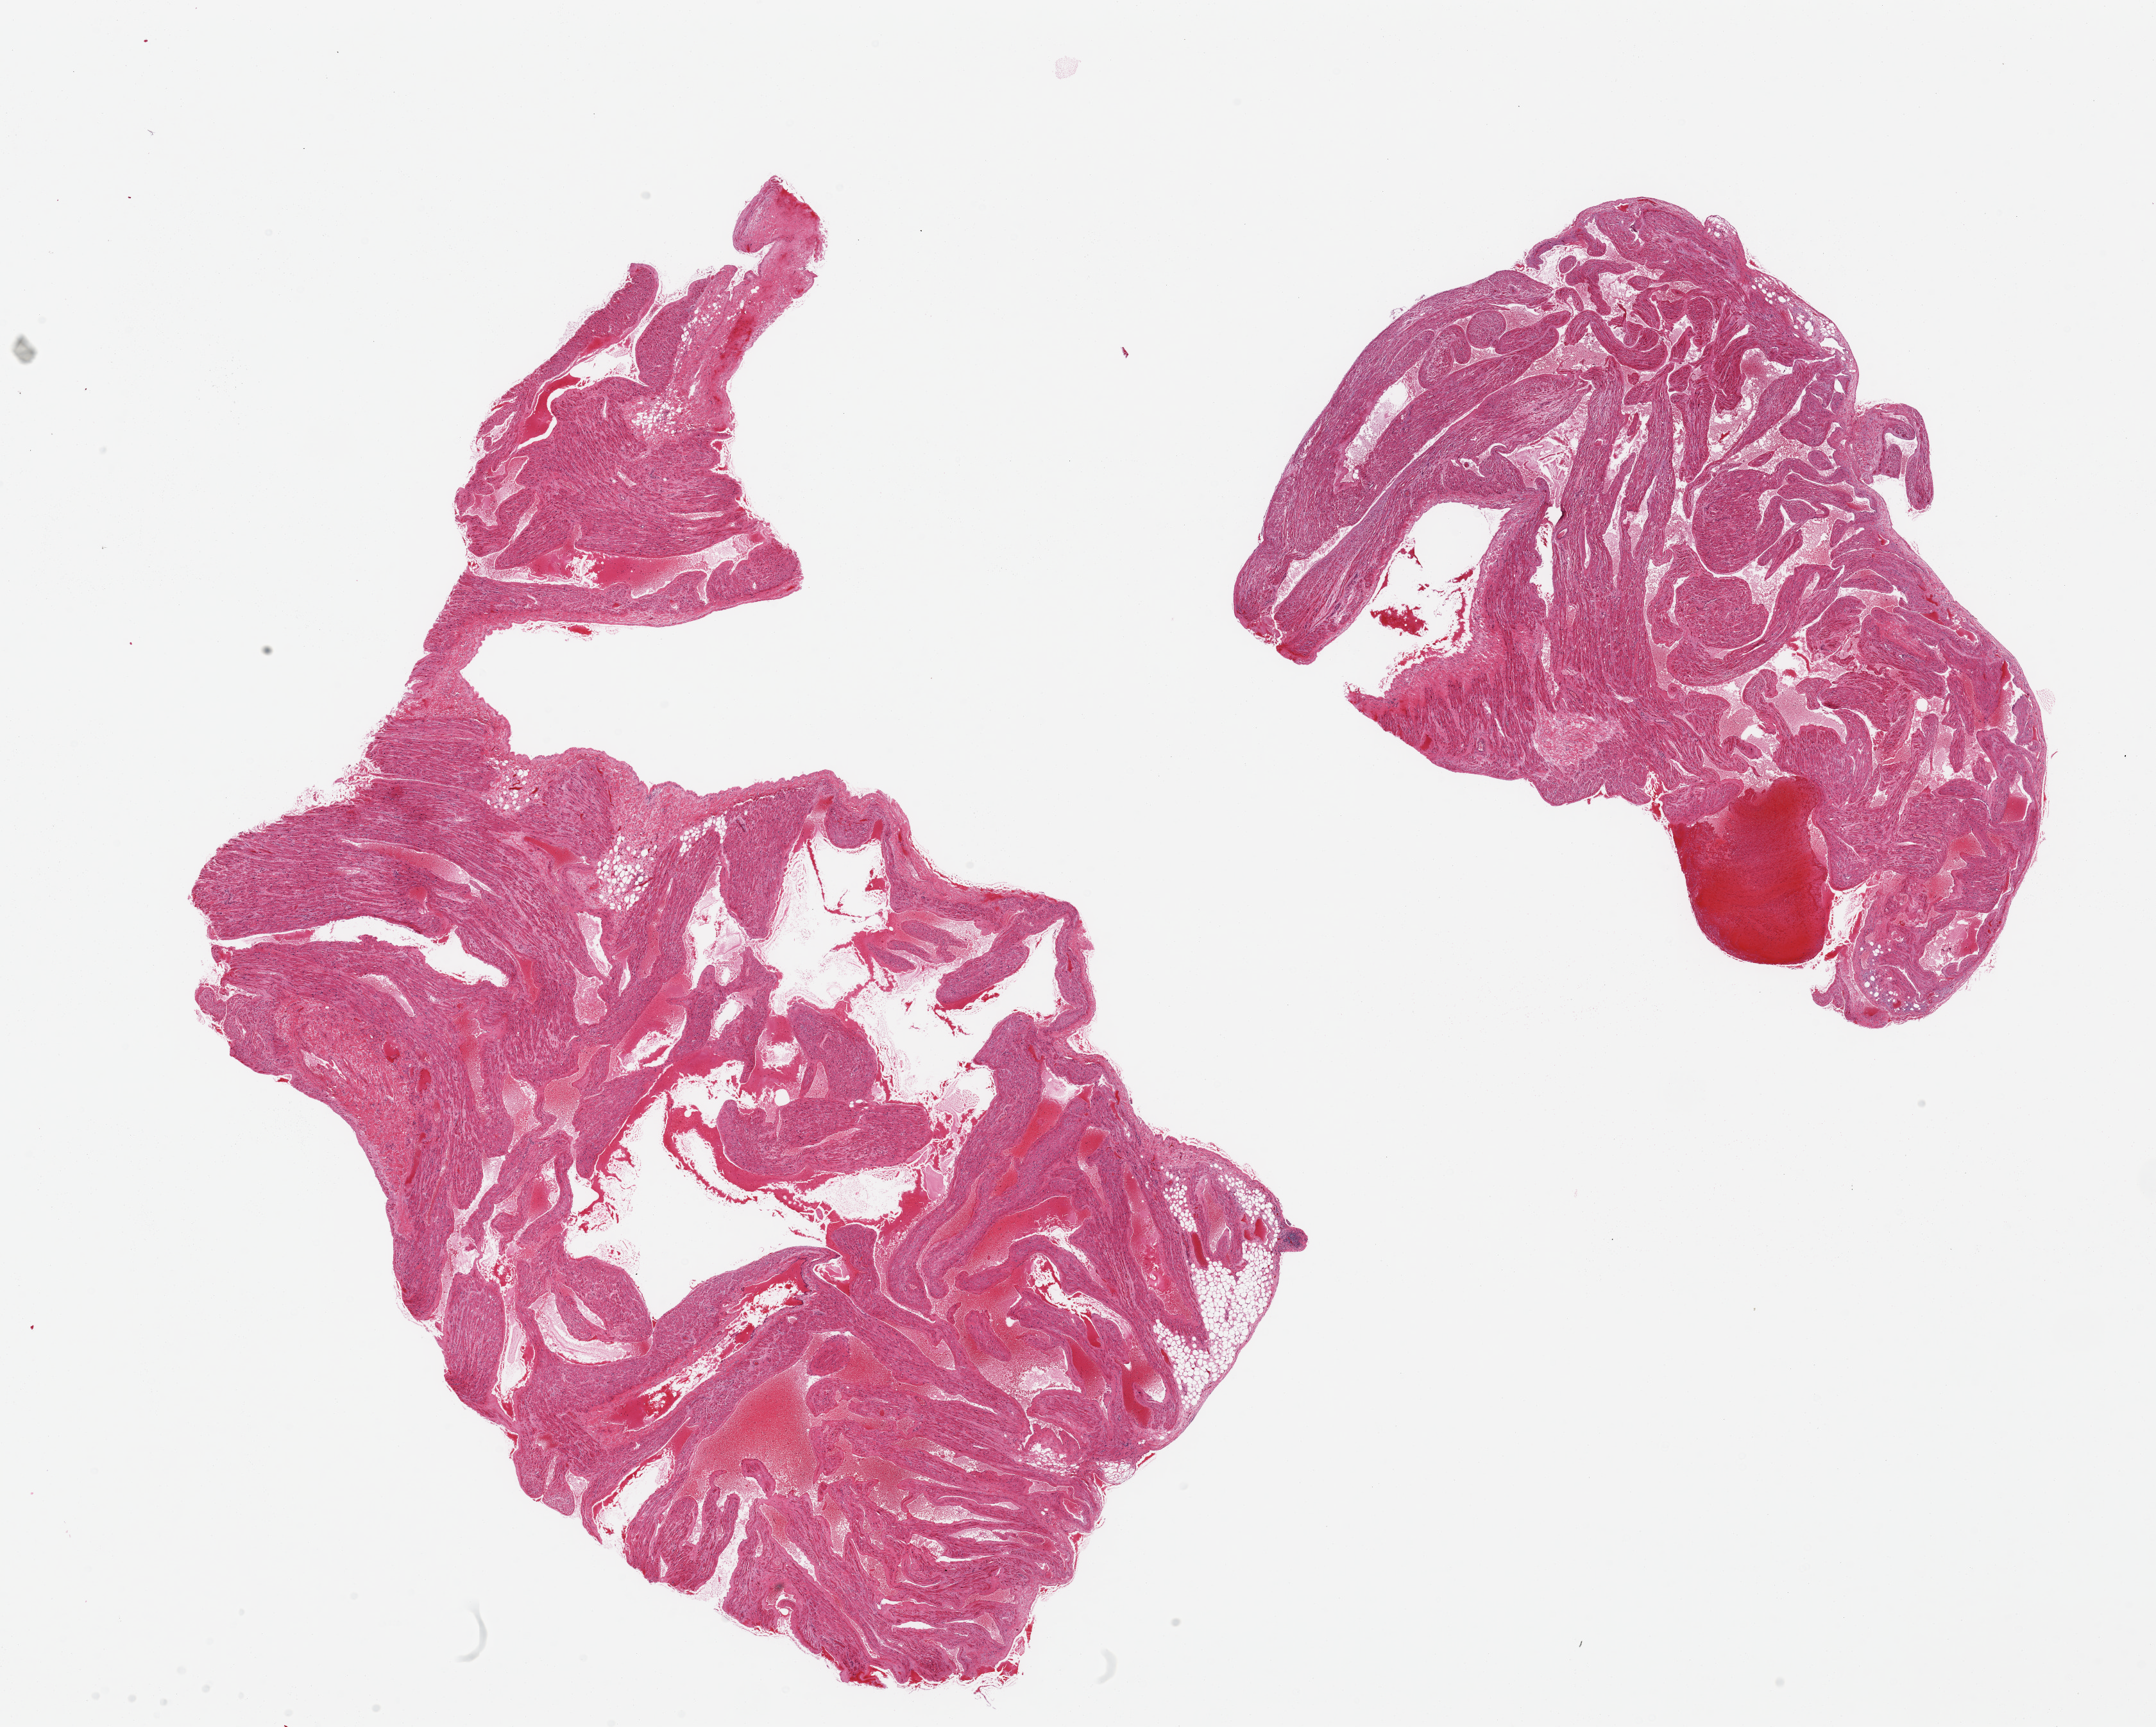
Digitized hematoxylin and eosin (H&E)-stained section, low-resolution overview of the scanned area, about 26.6 x 21.3 mm (slide scanned at 20x); PAXgene-fixed paraffin-embedded (PFPE) section; target tissue: auricular appendage; donor tissue sample. Donor sex: male.
• reviewer comment on this tissue sample: 2 pieces, no abnormalities